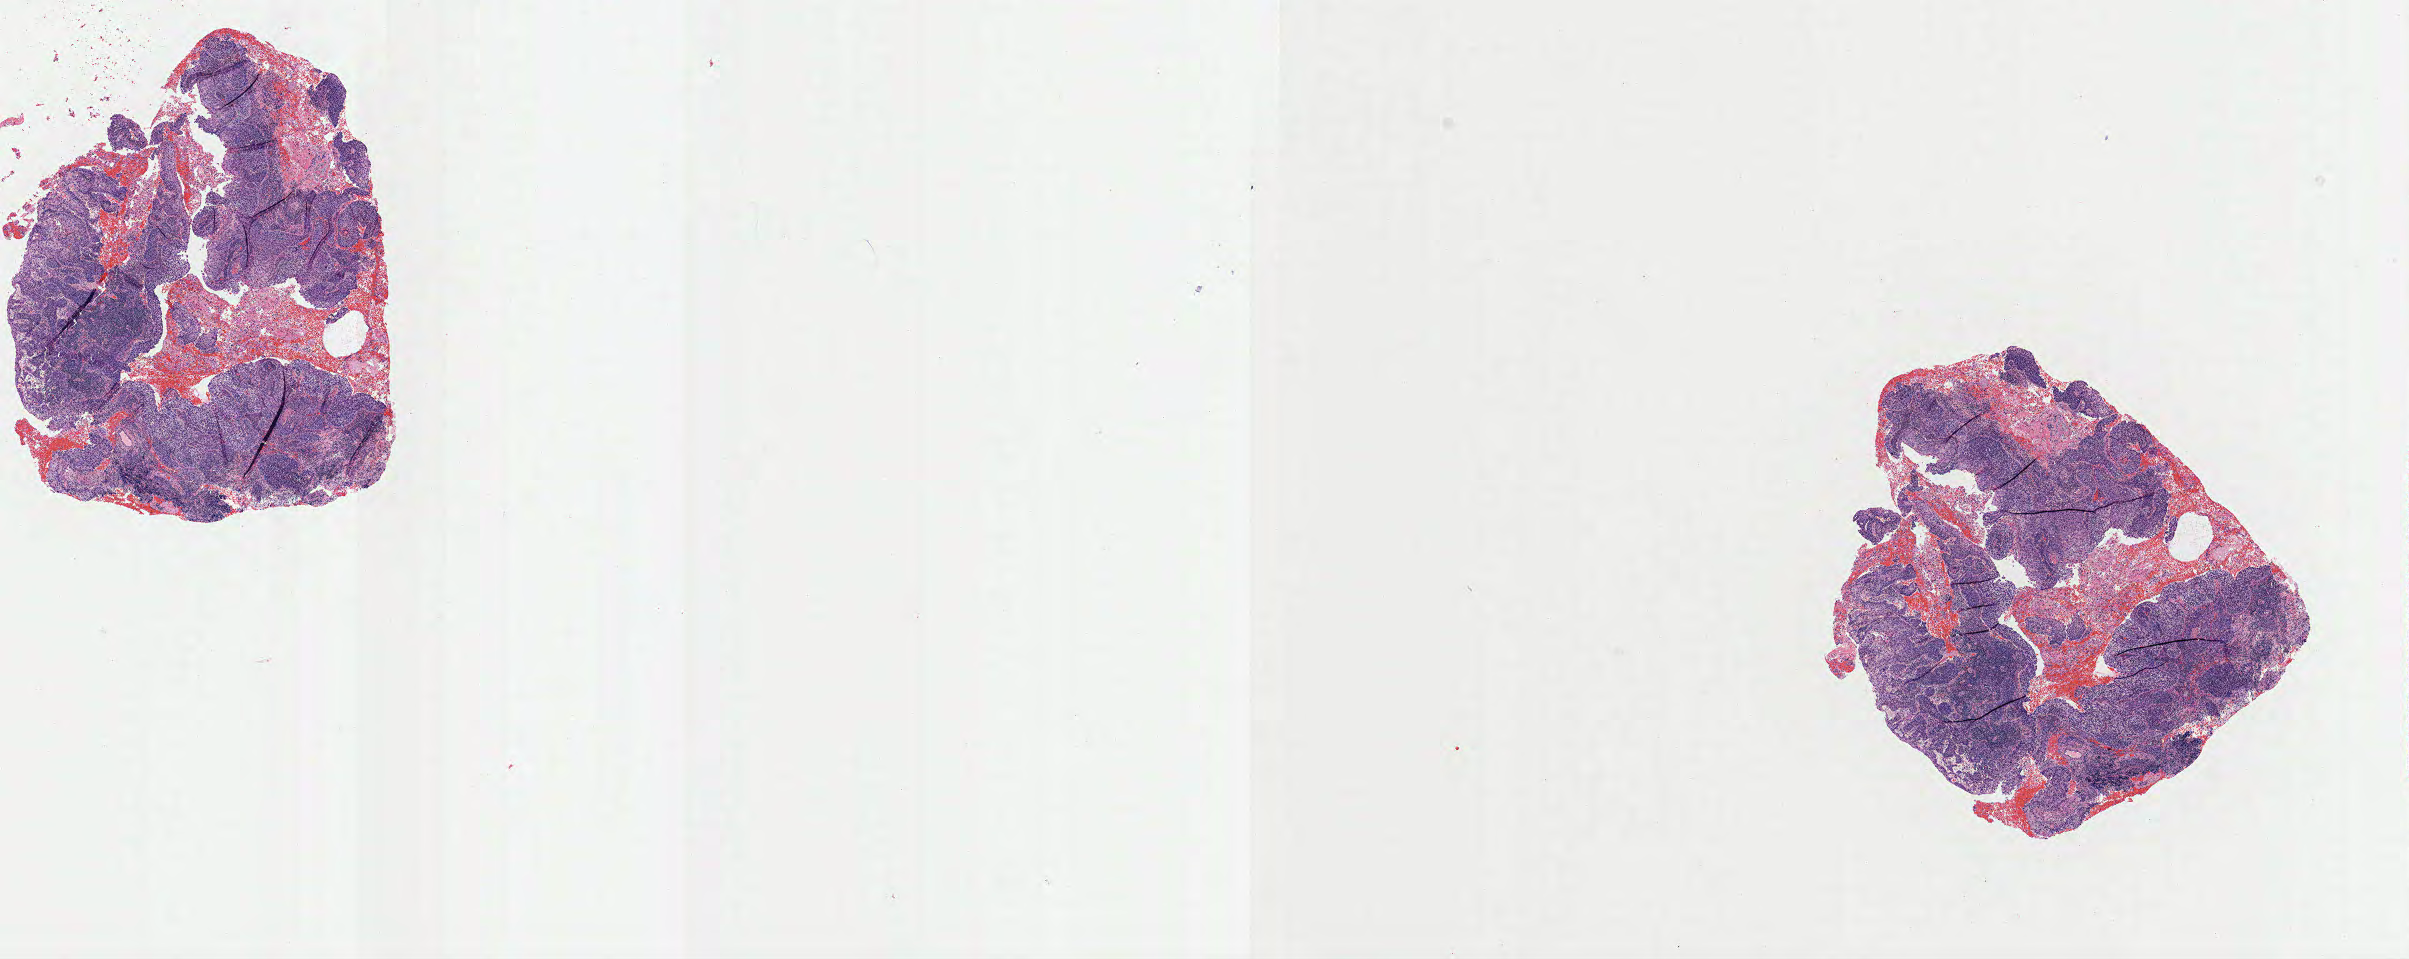
Whole-slide image, H&E stain — shown as a low-resolution overview of the whole scanned area (about 19.0 x 7.6 mm). Tumor tissue. Anatomic site: cervix. Female patient, age 60 years.
- histologic diagnosis: Squamous cell carcinoma, keratinizing, NOS